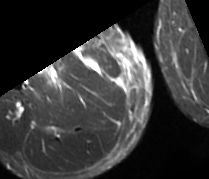
MRI of an extremity soft-tissue mass, one axial slice; STIR; MR volume resampled by the dataset authors to the PET/CT grid (not the native acquisition matrix); 3.27 mm slice thickness; 209 × 179 image matrix, field of view 204 × 175 mm. Male patient. From the clinical record (not read from this slice): histological type: undifferentiated - pleiomorphic; grade: high; site of the primary tumour: right thigh.
Annotated regions visible in this slice (expert contour drawn on MRI and transferred to this co-registered scan by the dataset authors):
- gross tumour volume including surrounding oedema: bounding box [x1, y1, x2, y2] px = [43, 64, 61, 85]